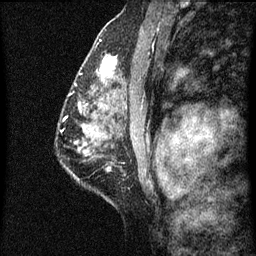
Breast MRI (dynamic contrast-enhanced), one sagittal slice. Position 41 of 60 along the scan axis. Dynamic contrast-enhanced series, image 2 of 7 at this slice position (ordered by acquisition). 1.5 T. TE 4.2 ms, TR 8 ms. 2 mm slice thickness. 256 × 256 image matrix. Patient: female, 51 years.
Outlined on this slice (semi-automatically segmented with operator editing):
- analysis volume of interest (the breast-tissue region the enhancement analysis was run in; not a lesion): bounding box <86,48,125,101> (left, top, right, bottom; pixels)
- tumour enhancement mask (voxels above the 70 % enhancement threshold inside the analysis volume of interest): <101,56,118,77>